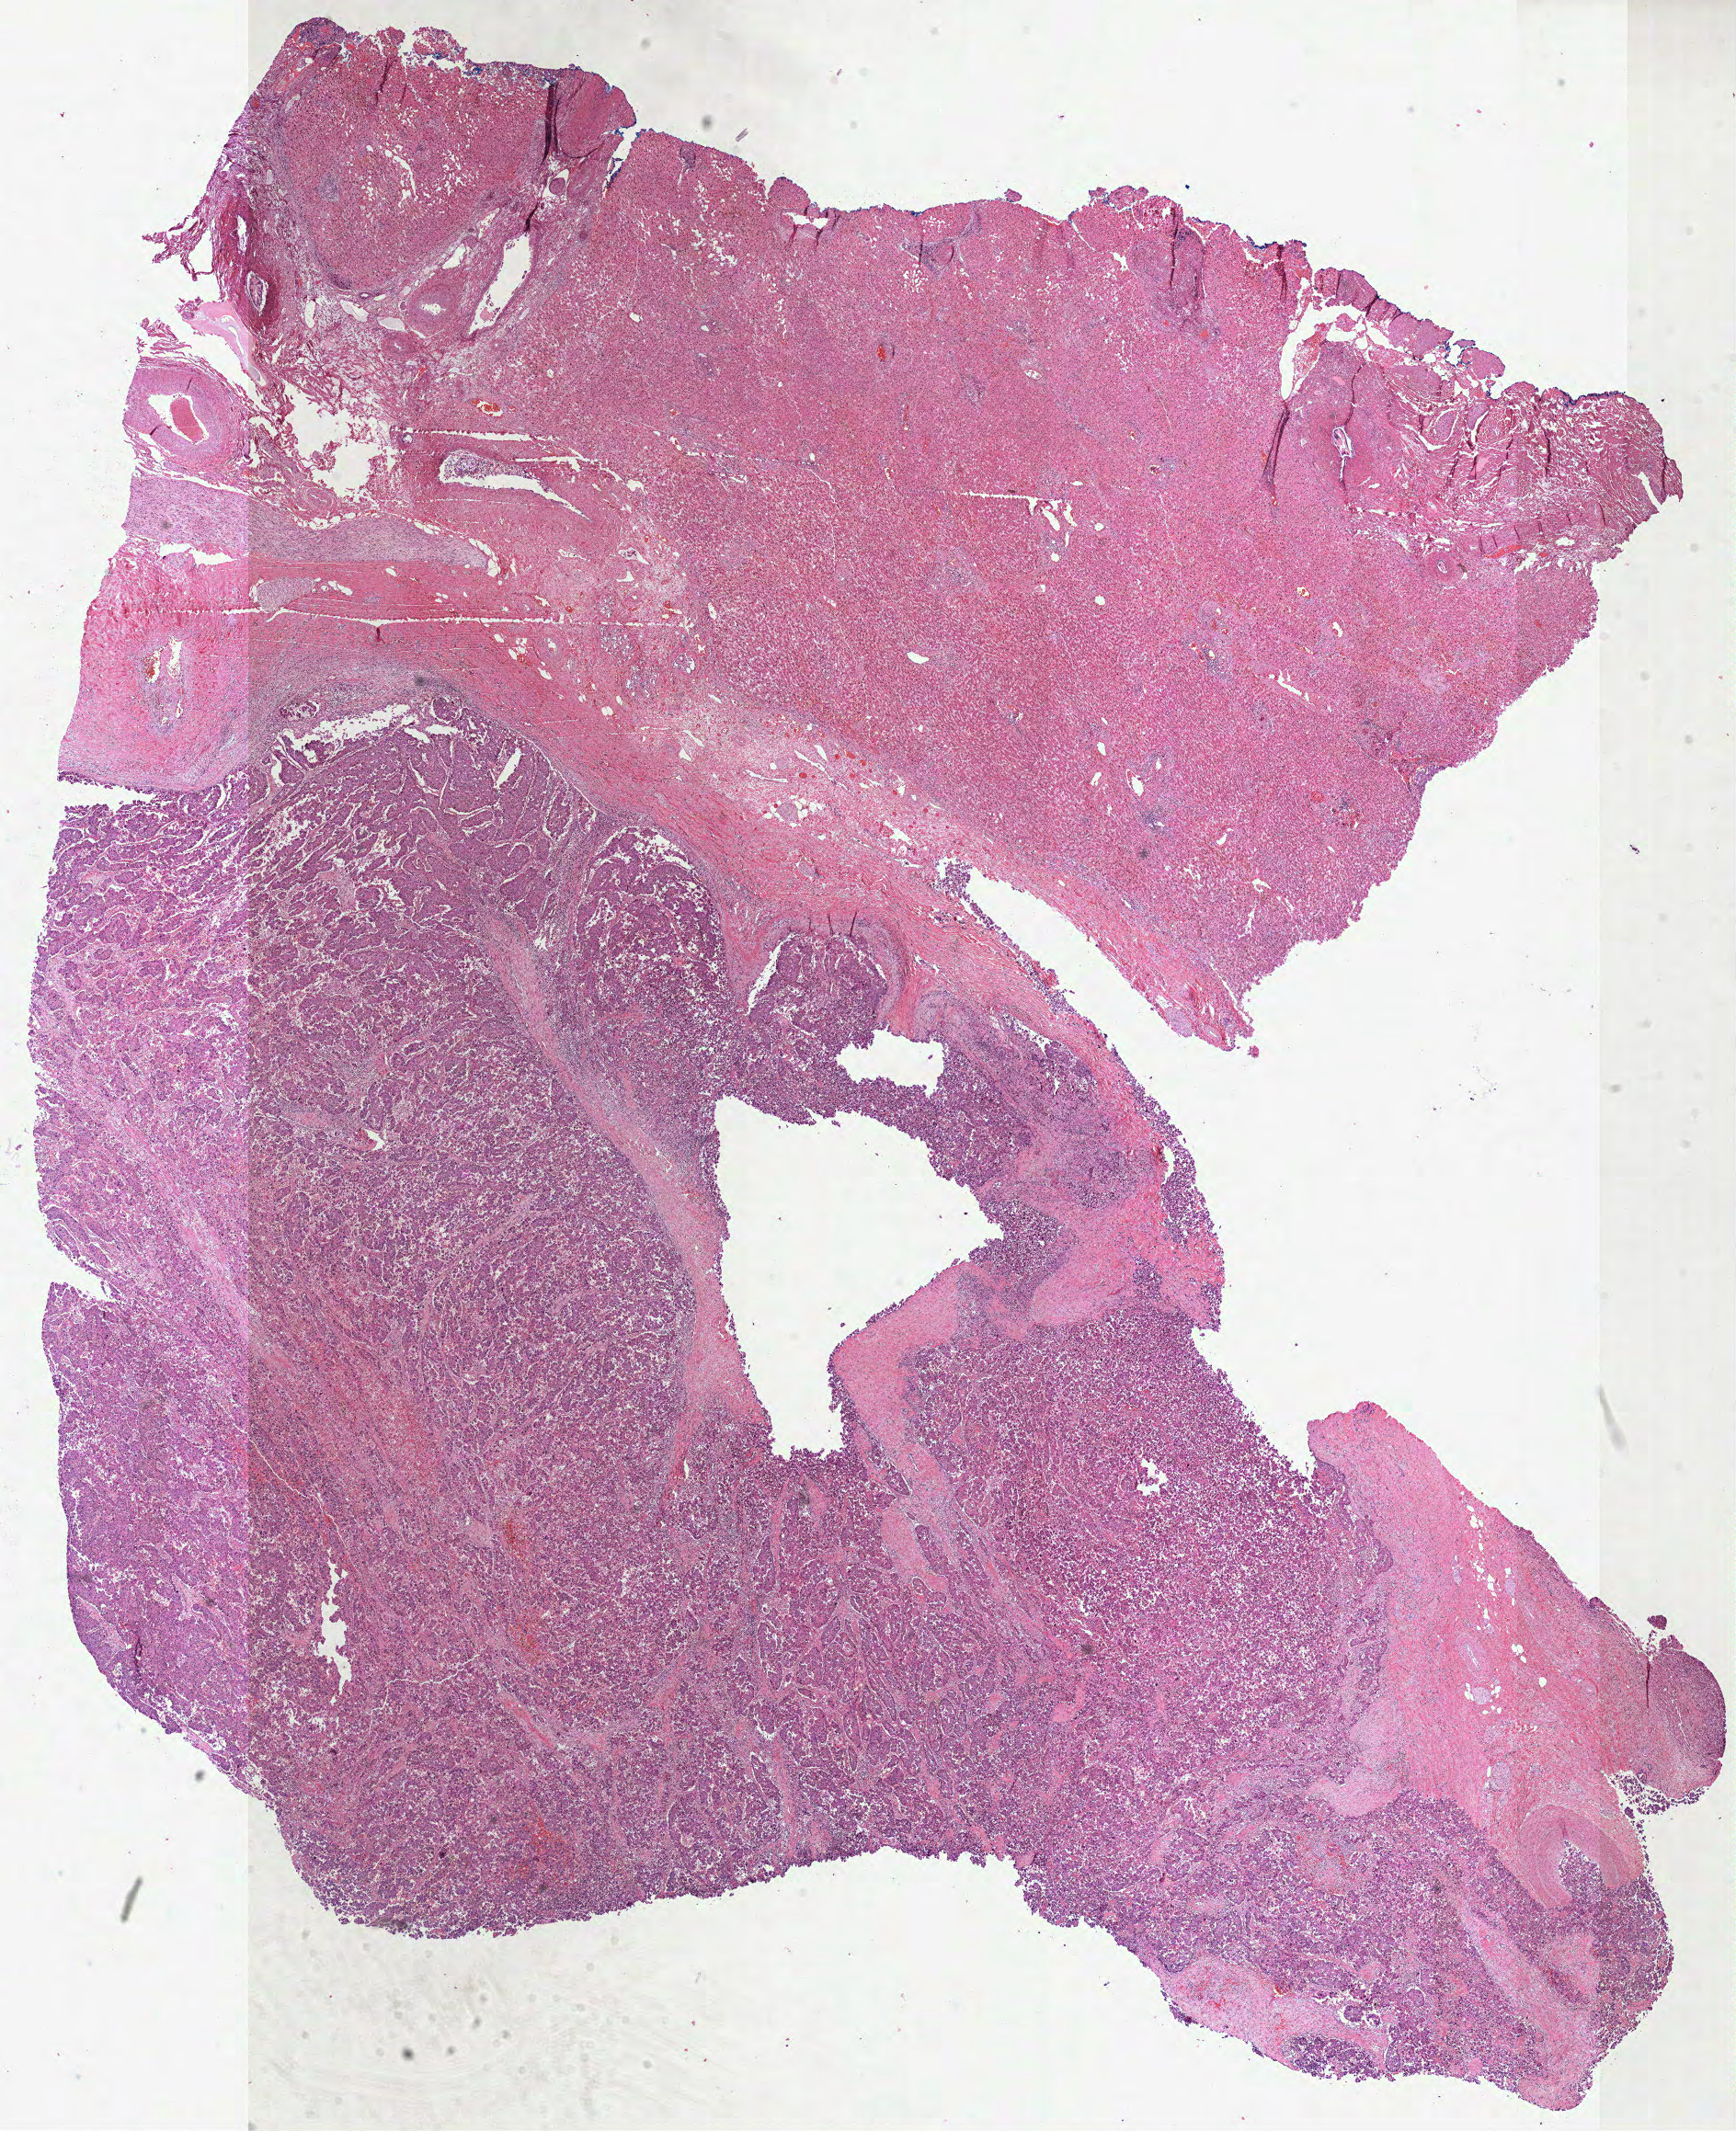
H&E-stained whole-slide image, low-resolution overview of the scanned area, about 15.2 x 18.7 mm (acquisition: 40x scan); formalin-fixed paraffin-embedded (FFPE) diagnostic section; sample: primary tumour, liver. Male patient; age at initial diagnosis 78 years. Histologic grade: G2 (moderately differentiated).
• diagnosis: Hepatocellular carcinoma, NOS
• AJCC pathologic stage: IIIA